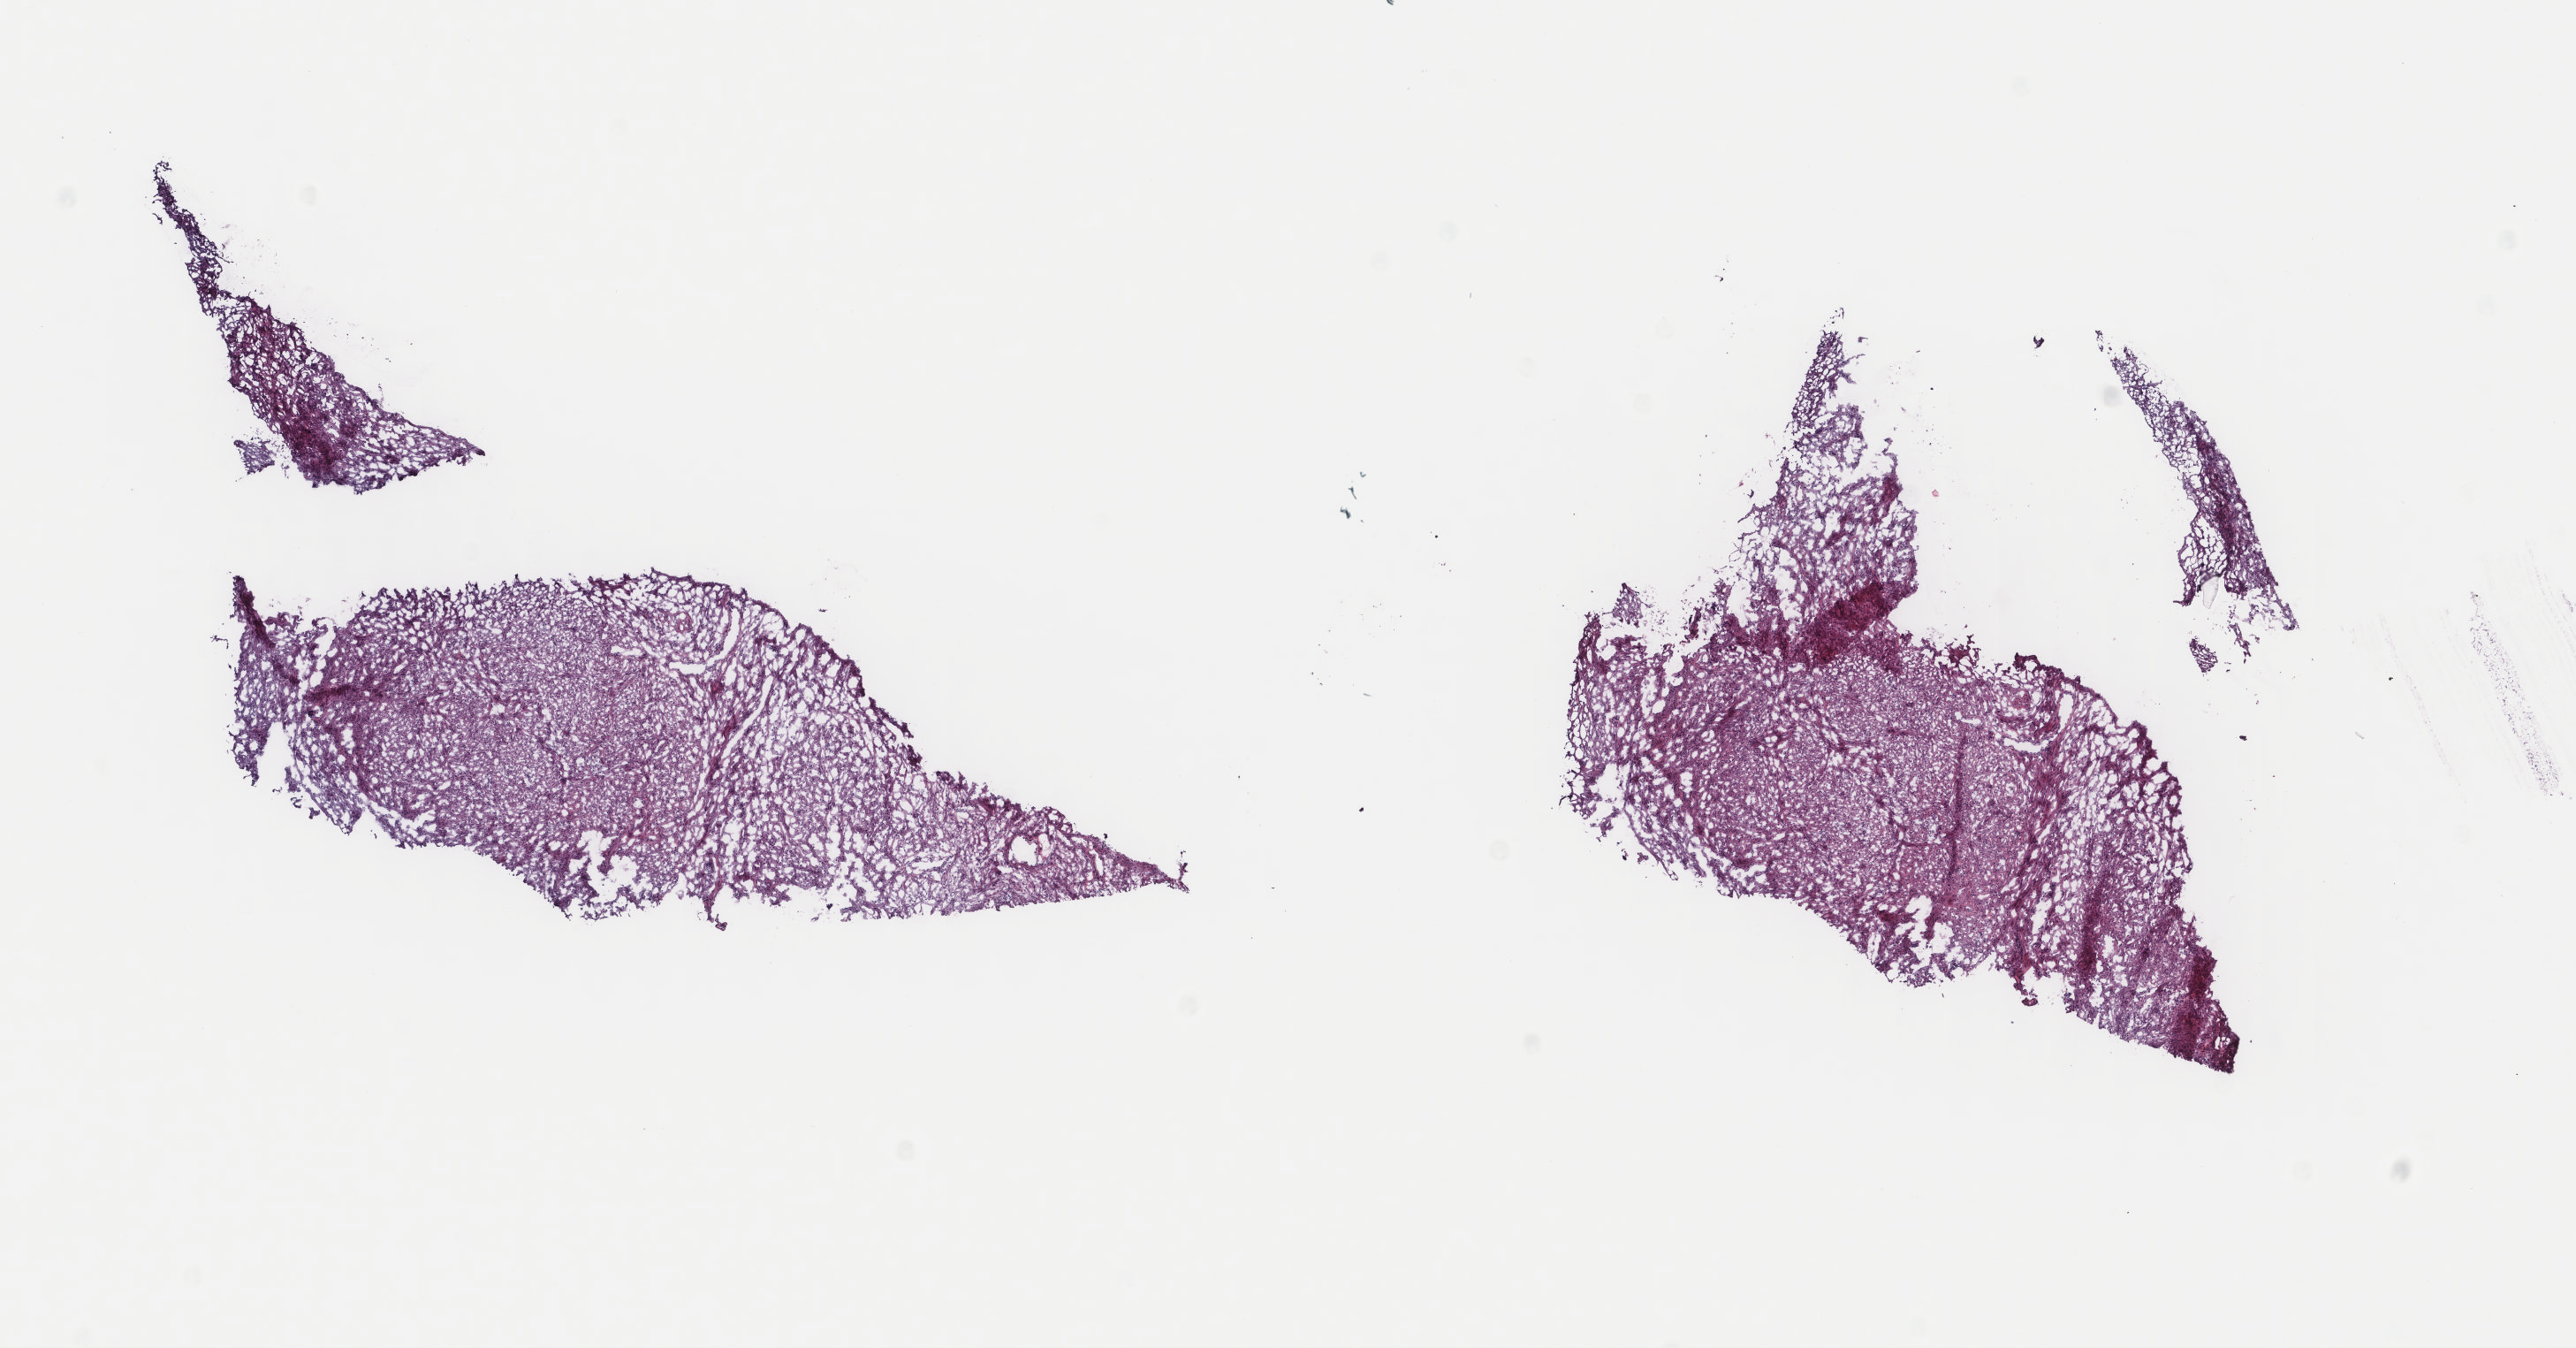
Whole-slide histology image, H&E — low-resolution overview of the scanned area, about 11.6 x 6.1 mm (from a 40x scan); frozen section from the top of the tissue portion; primary tumour sample from the meninges. Female, age 62 years at initial diagnosis. Composition of this section per pathologist review: tumour cells 100%, tumour nuclei 80%.
Pathologic diagnosis: Malignant peripheral nerve sheath tumor (spinal meninges).